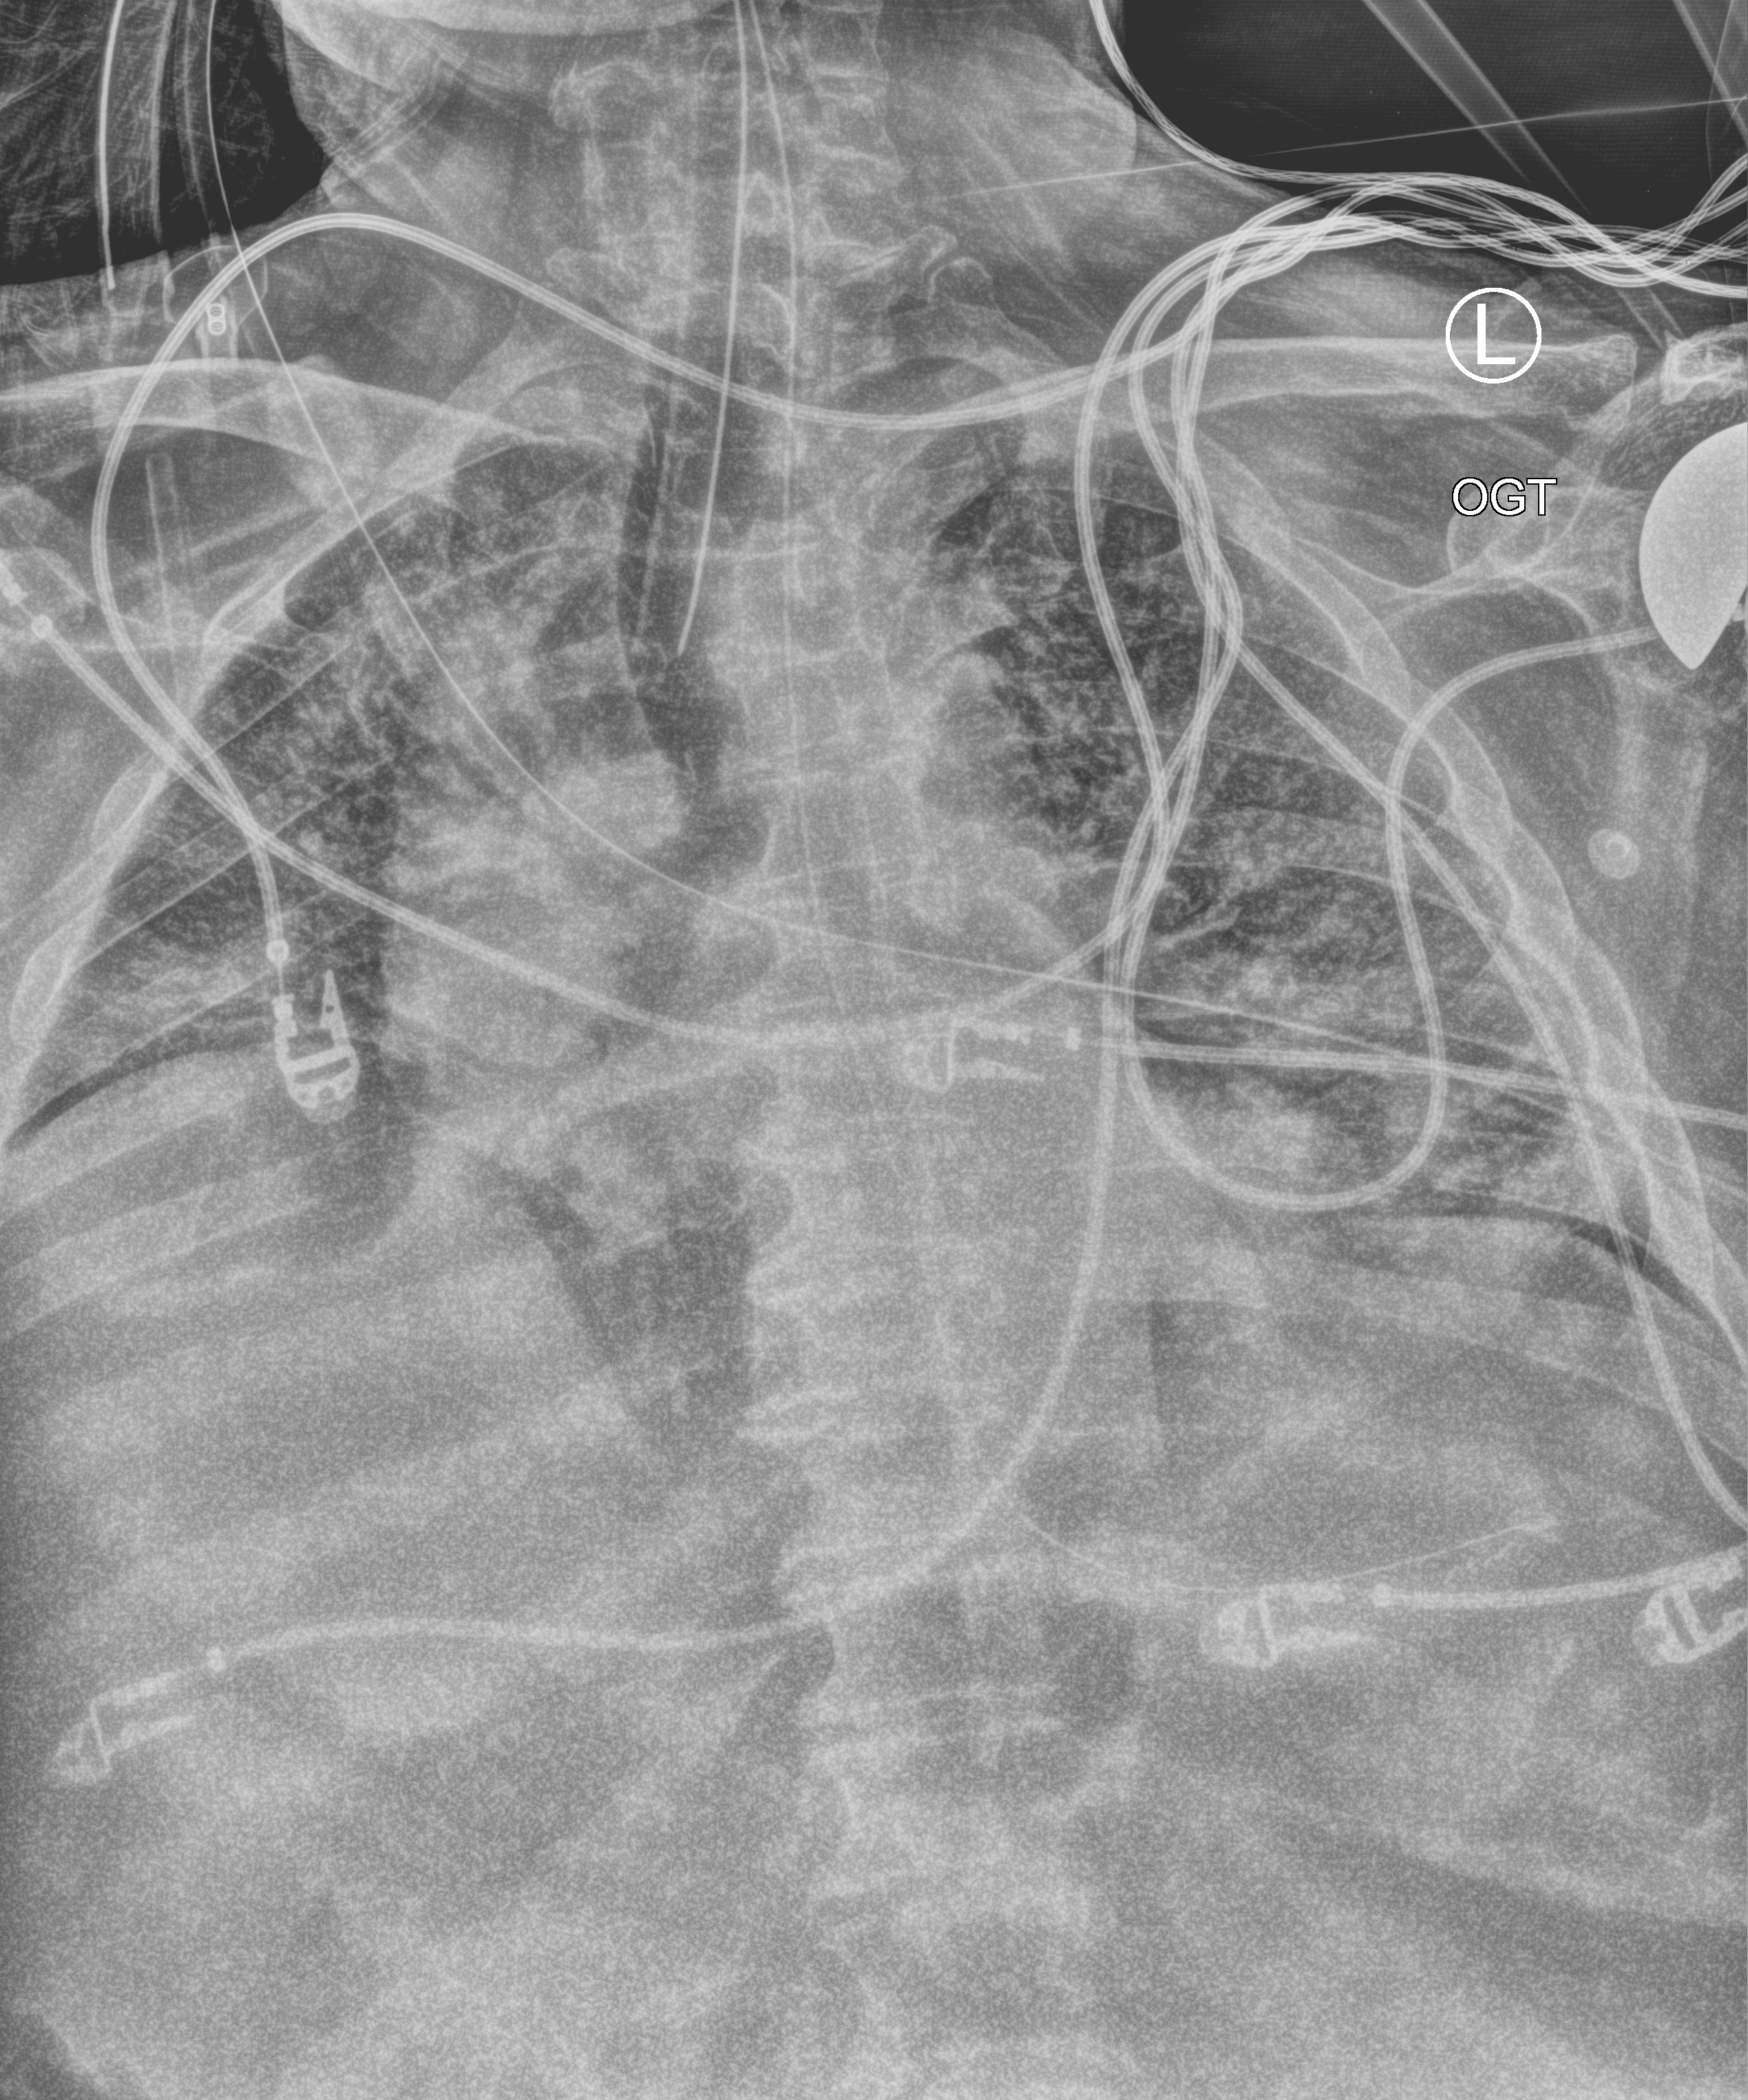
Chest X-ray (portable), anteroposterior (AP) projection. Patient hospitalised with COVID-19; male, aged 60–74 years.
Hospital-stay facts (about this admission, not read from this image; timing relative to this image not recorded): admitted to intensive care during this hospital stay: yes.